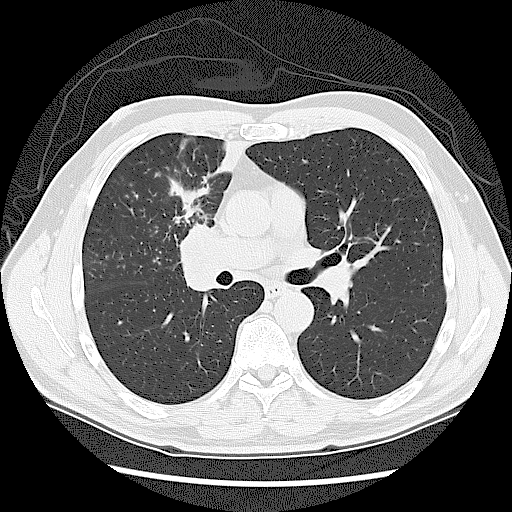
Chest CT (low-dose screening protocol), one axial image. First (baseline) screen. Lung window (W 1500 / L -600 HU). Slice 60 of 131 in the series. Male, age 60 years at enrolment. Current smoker at enrolment.
Expert reader's lesion annotation, bounding box <158,216,240,306> (left, top, right, bottom; pixels). Screening reader's record for this exam: no non-calcified nodule ≥4 mm recorded. Later outcome: lung cancer diagnosed 41 days after this screen — small cell carcinoma, NOS, right upper lobe, stage IIIA (AJCC 6th edition).